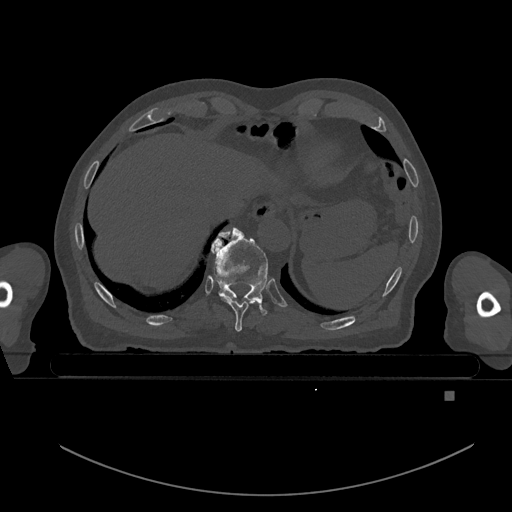
CT including the spine, one axial slice. Slice 115 of 969 in the series (ordered by position). Bone window (W 1800 / L 400 HU). 0.5 mm slice thickness. 512 × 512 image matrix, field of view 456 × 456 mm. Male patient, age 82 years. Case-level facts recorded for this patient, not image findings: primary cancer: prostate; vertebrae with lytic lesions (as recorded): T11, T9, T8, T2.
Outlined on this slice (semi-automatic segmentation, software-assisted and operator-edited):
- T10 vertebra: bounding box (x1, y1, x2, y2) in pixels: (211, 227, 269, 314)
- T9 vertebra: (219, 231, 259, 332)